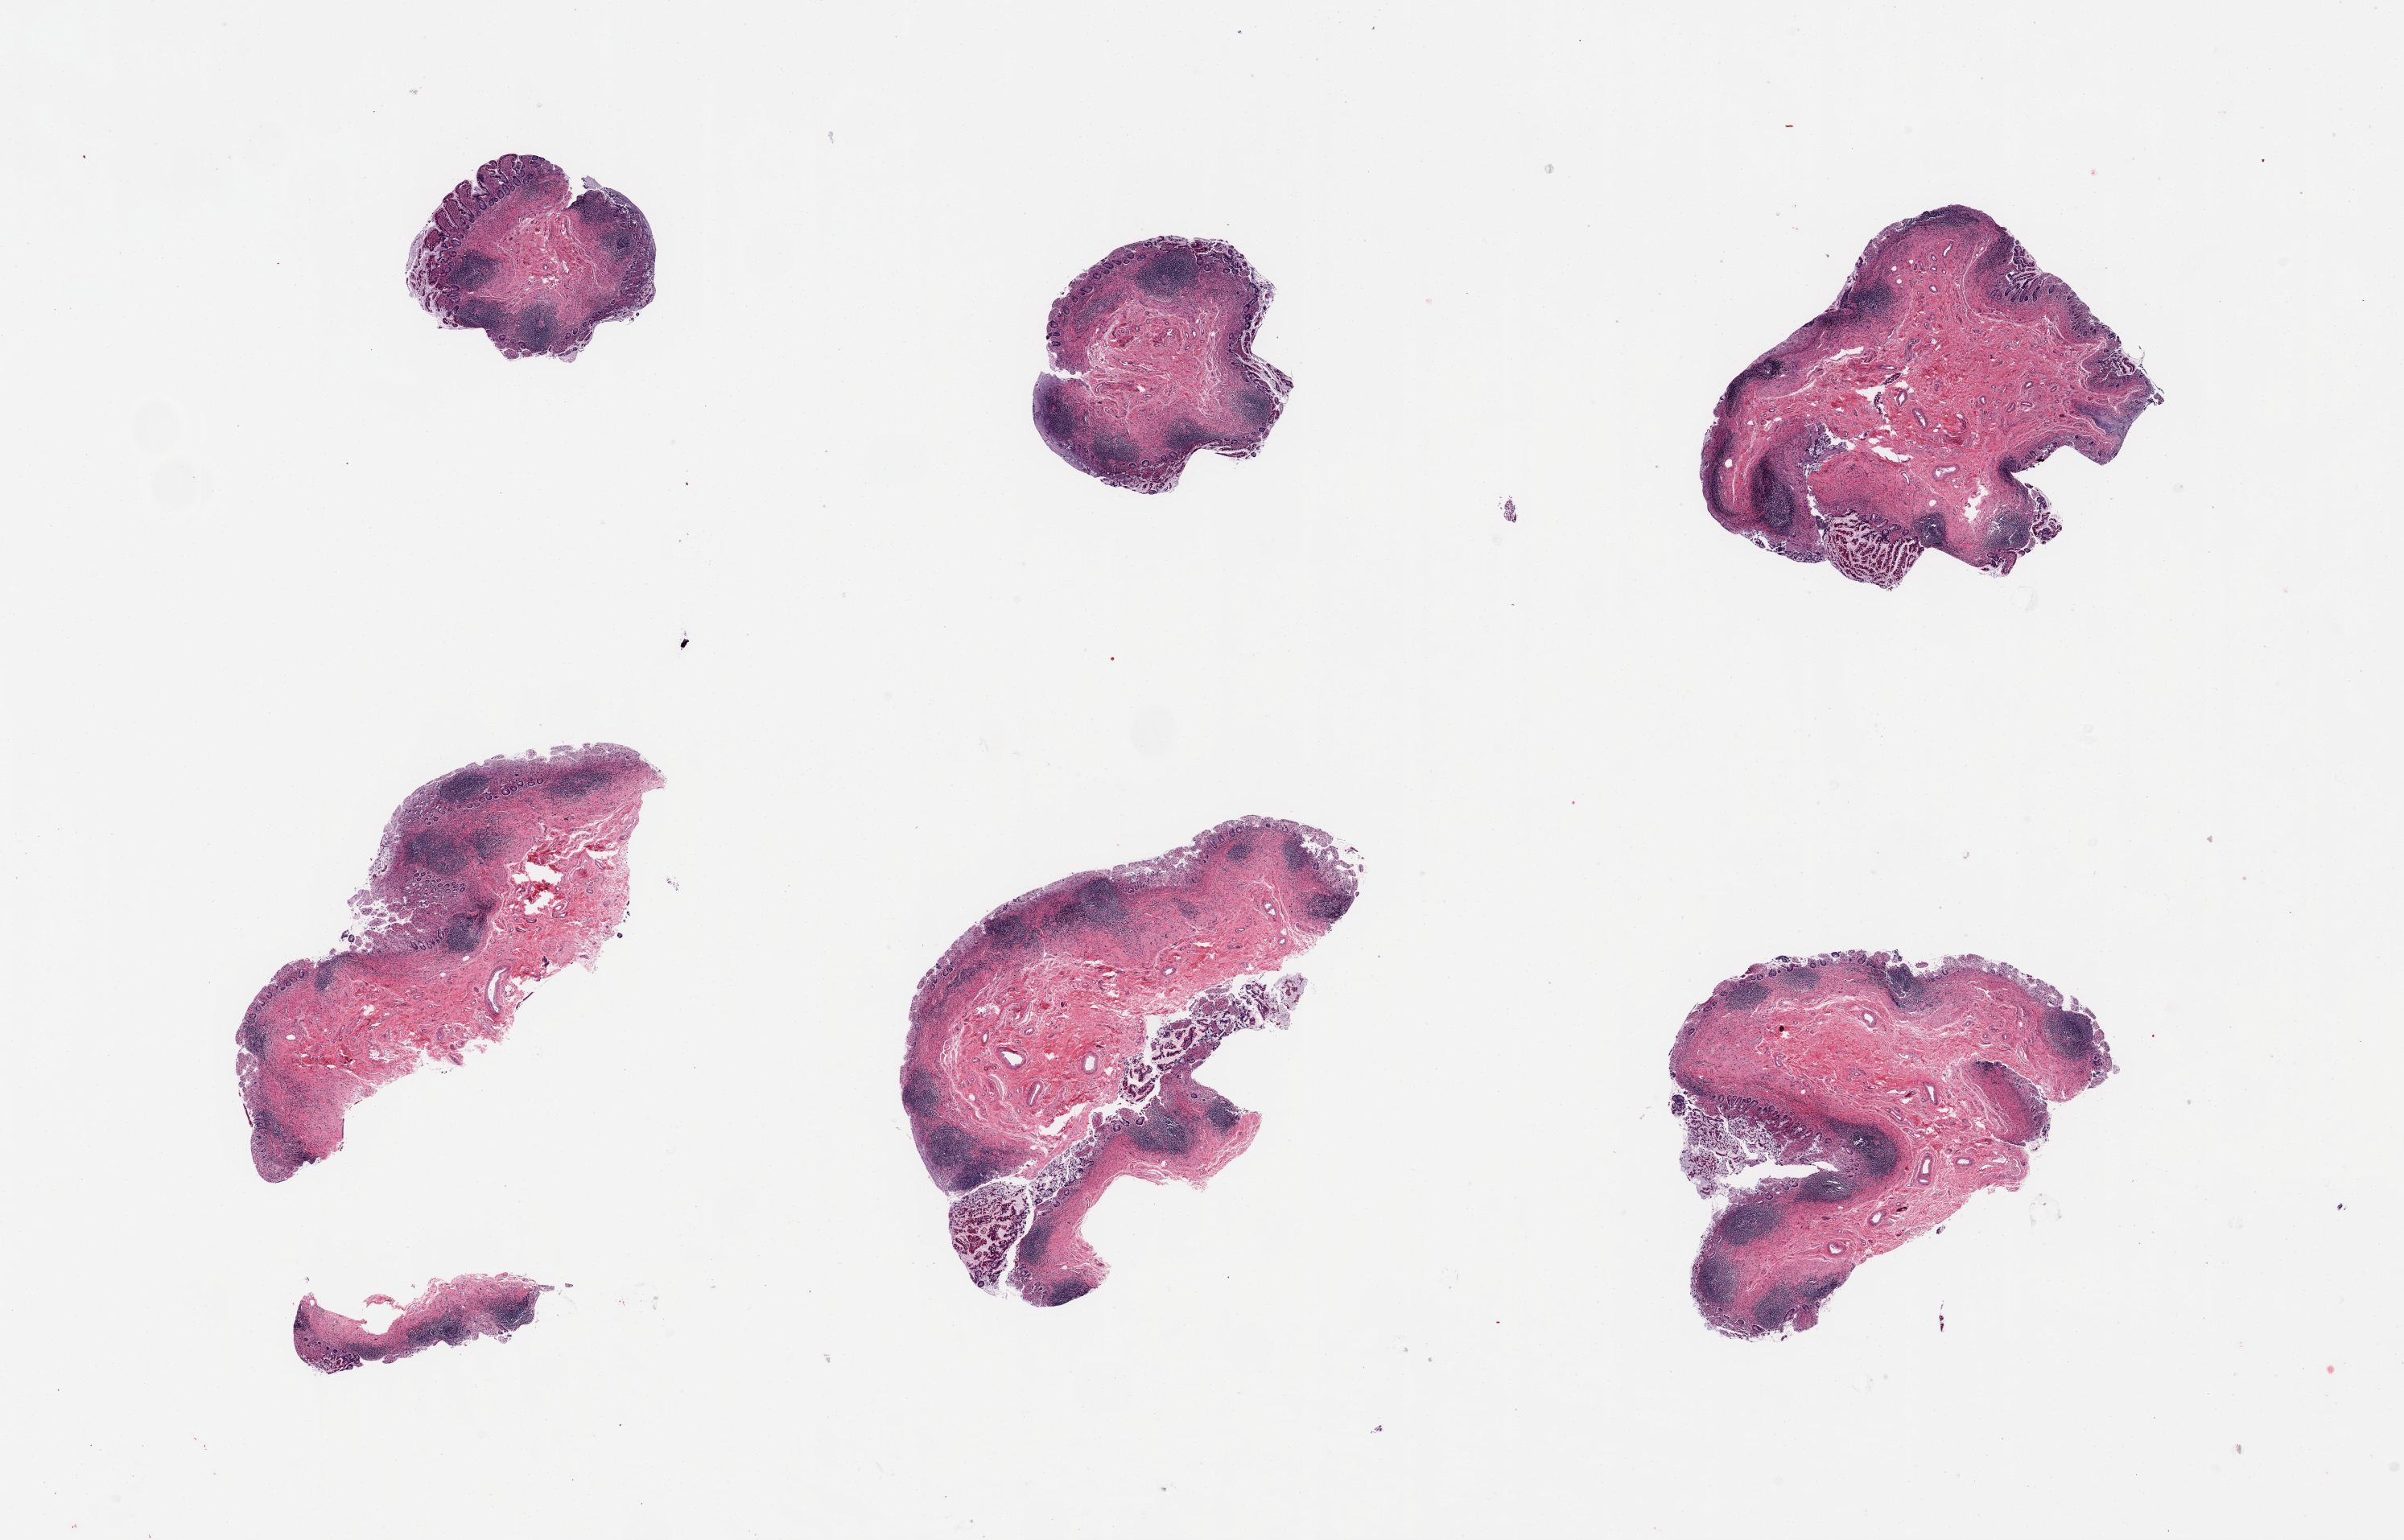
Digitized H&E-stained section, brightfield — whole scanned area (about 23.6 x 15.1 mm) shown as a low-resolution overview.
Specimen: PAXgene-fixed, paraffin-embedded tissue; sampled site (target tissue): ileum; tissue donor sample.